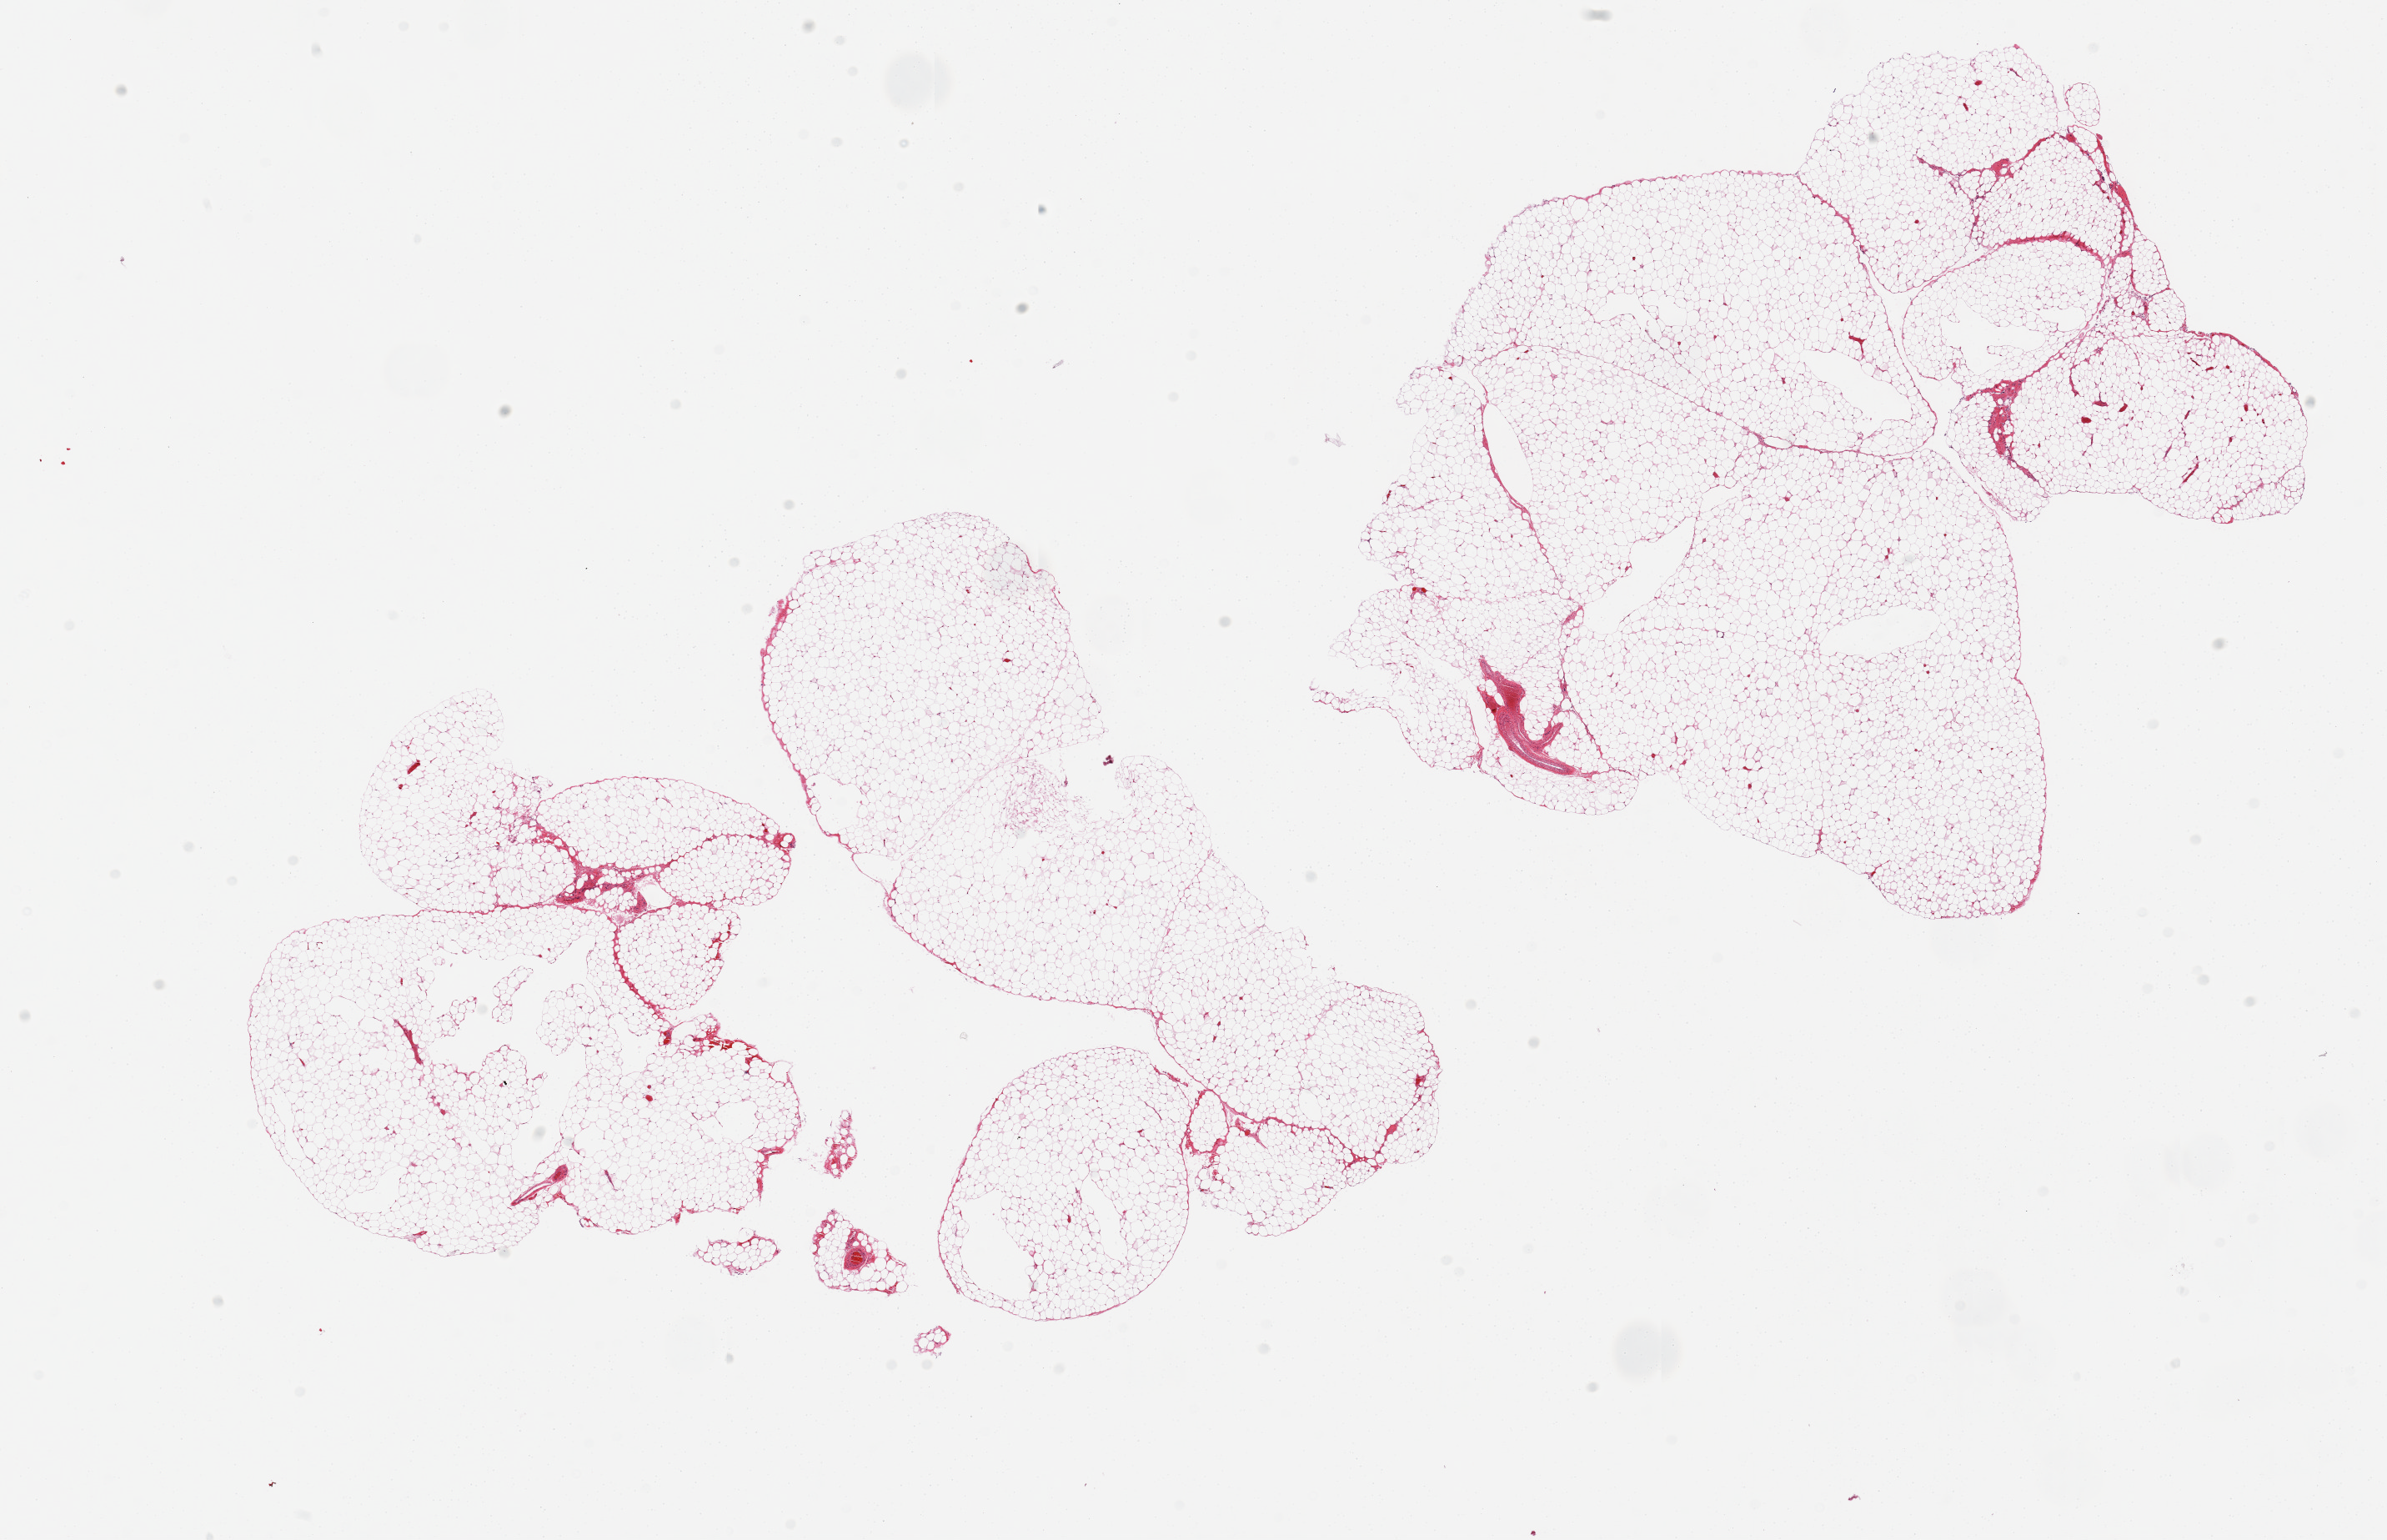
Digitized H&E-stained section, brightfield, a low-resolution overview of the entire scanned area, about 22.6 x 14.6 mm, PAXgene-fixed paraffin-embedded (PFPE) section, sampled site (target tissue): omentum, tissue donor sample. Male donor.
- pathologist's review note for this sample: 2 pieces